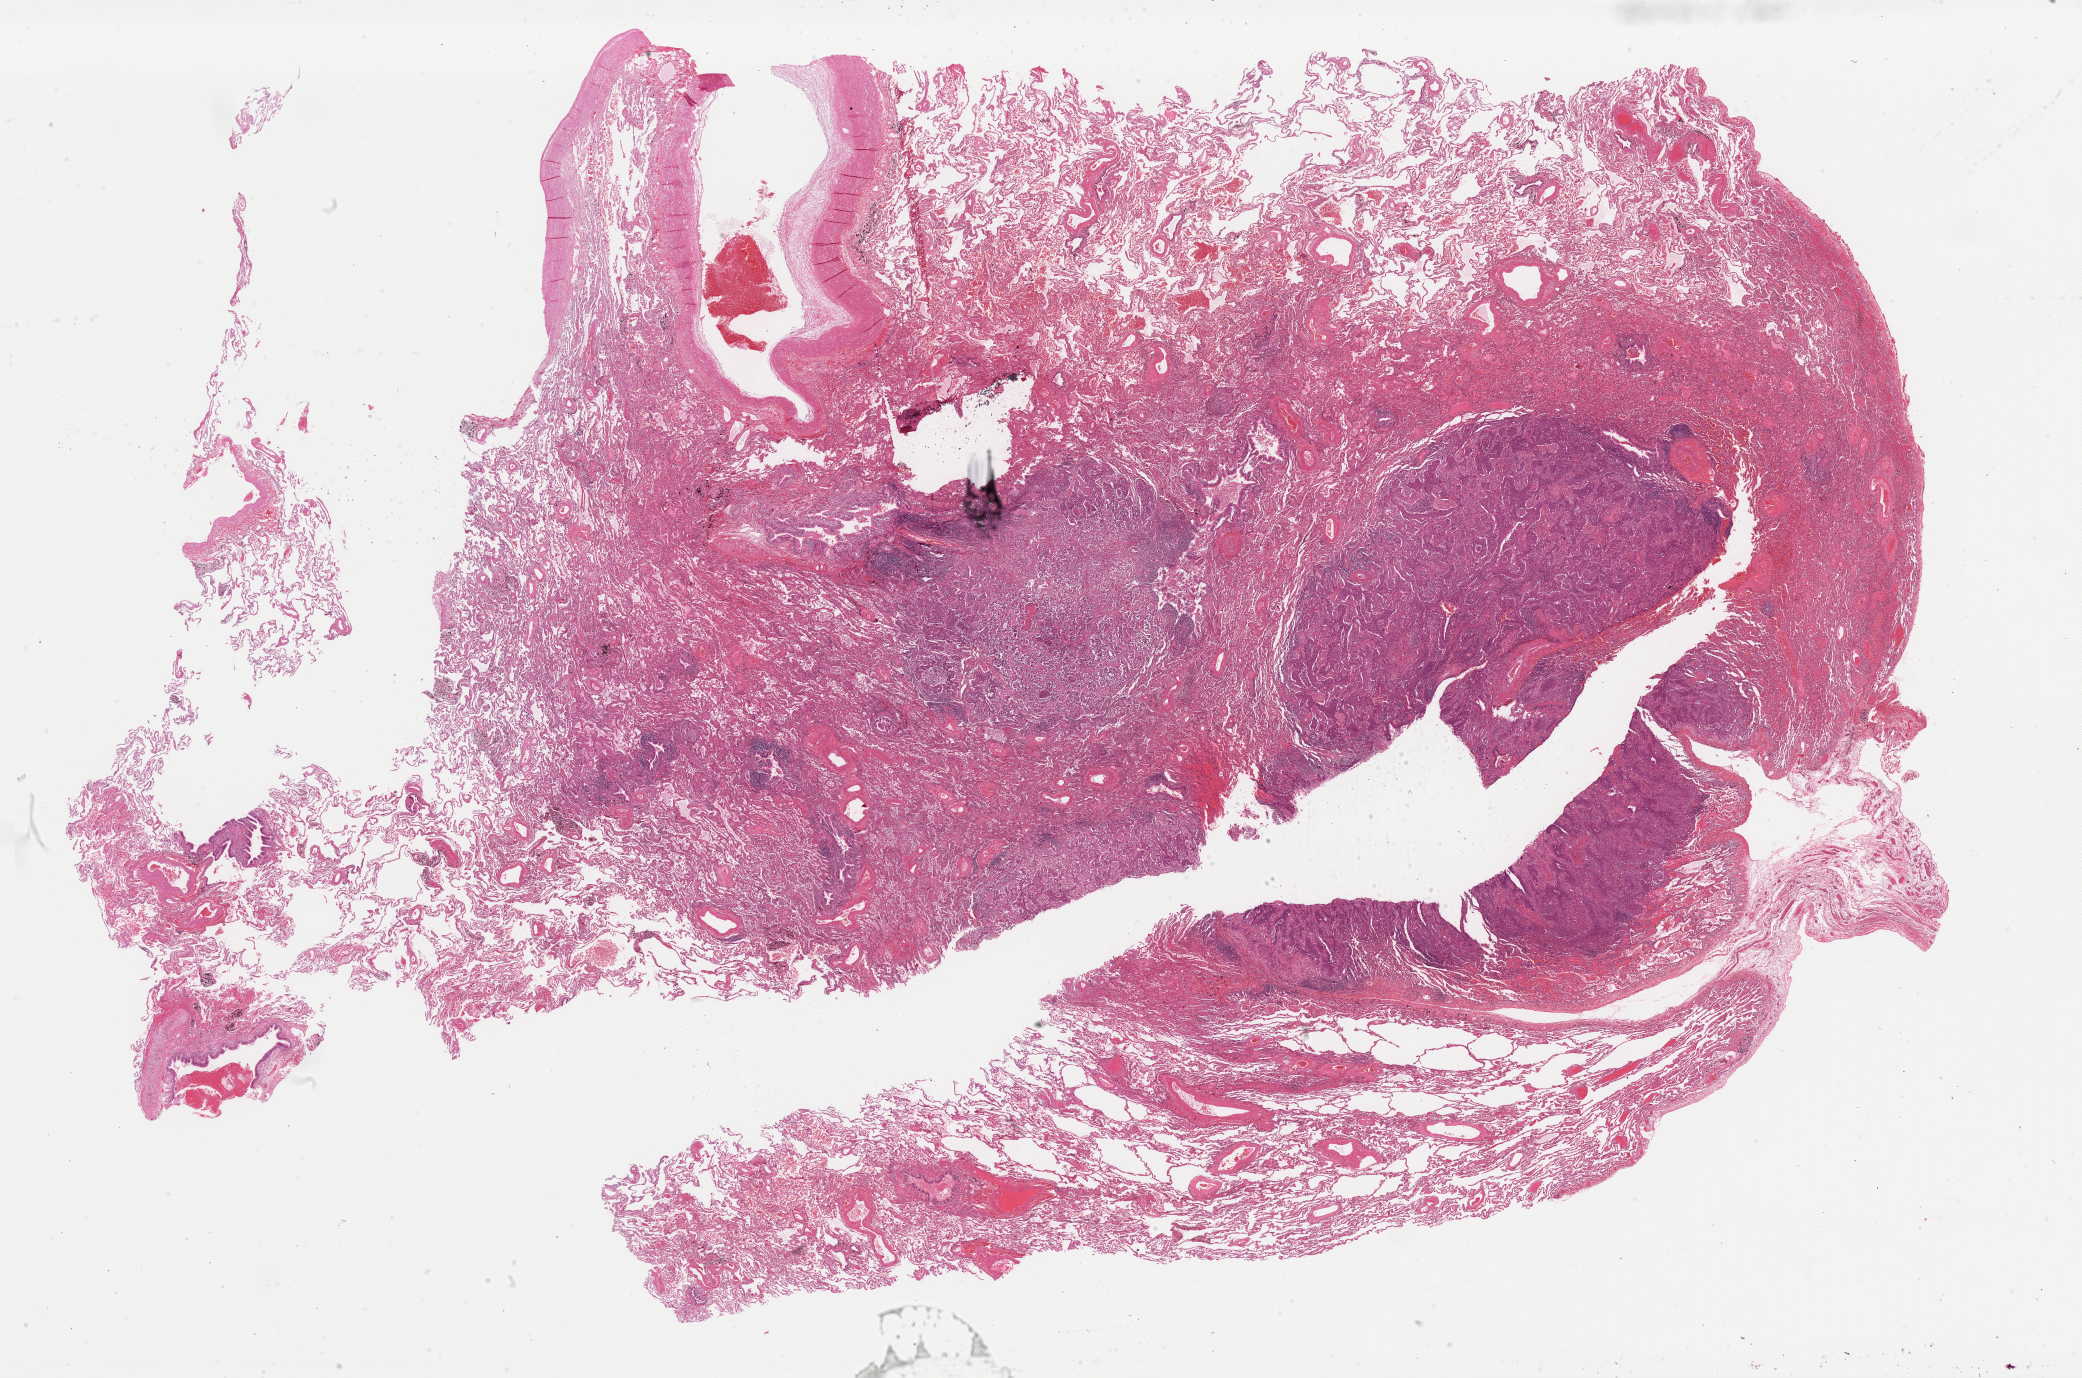
Hematoxylin and eosin (H&E) stained whole-slide image — whole scanned area (about 32.9 x 21.8 mm) shown as a low-resolution overview. Formalin-fixed paraffin-embedded (FFPE) diagnostic section. Primary tumour sample from the lung. Patient: male, age at initial diagnosis 81 years.
• AJCC pathologic stage: IB (7th edition)
• pathologic diagnosis: Squamous cell carcinoma, NOS (lower lobe, lung)
• laterality: left